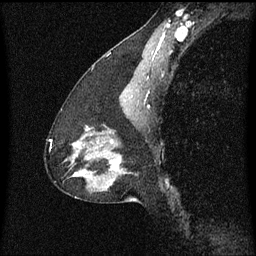
Breast MRI (dynamic contrast-enhanced), one sagittal slice; slice 36 of 60 in the series (ordered by position); dynamic contrast-enhanced series, image 2 of 3 at this slice position (ordered by acquisition); 1.5 T; TE 4.2 ms, TR 8.4 ms; 256 × 256 image matrix, field of view 200 × 200 mm. Female patient, age 47 years.
Structures marked on this image (semi-automatic segmentation, software-assisted and operator-edited):
- analysis volume of interest (the breast-tissue region the enhancement analysis was run in; not a lesion): bounding box (x1, y1, x2, y2) in pixels: (81, 140, 129, 191)
- tumour enhancement mask (voxels above the 70 % enhancement threshold inside the analysis volume of interest): (114, 166, 117, 169)